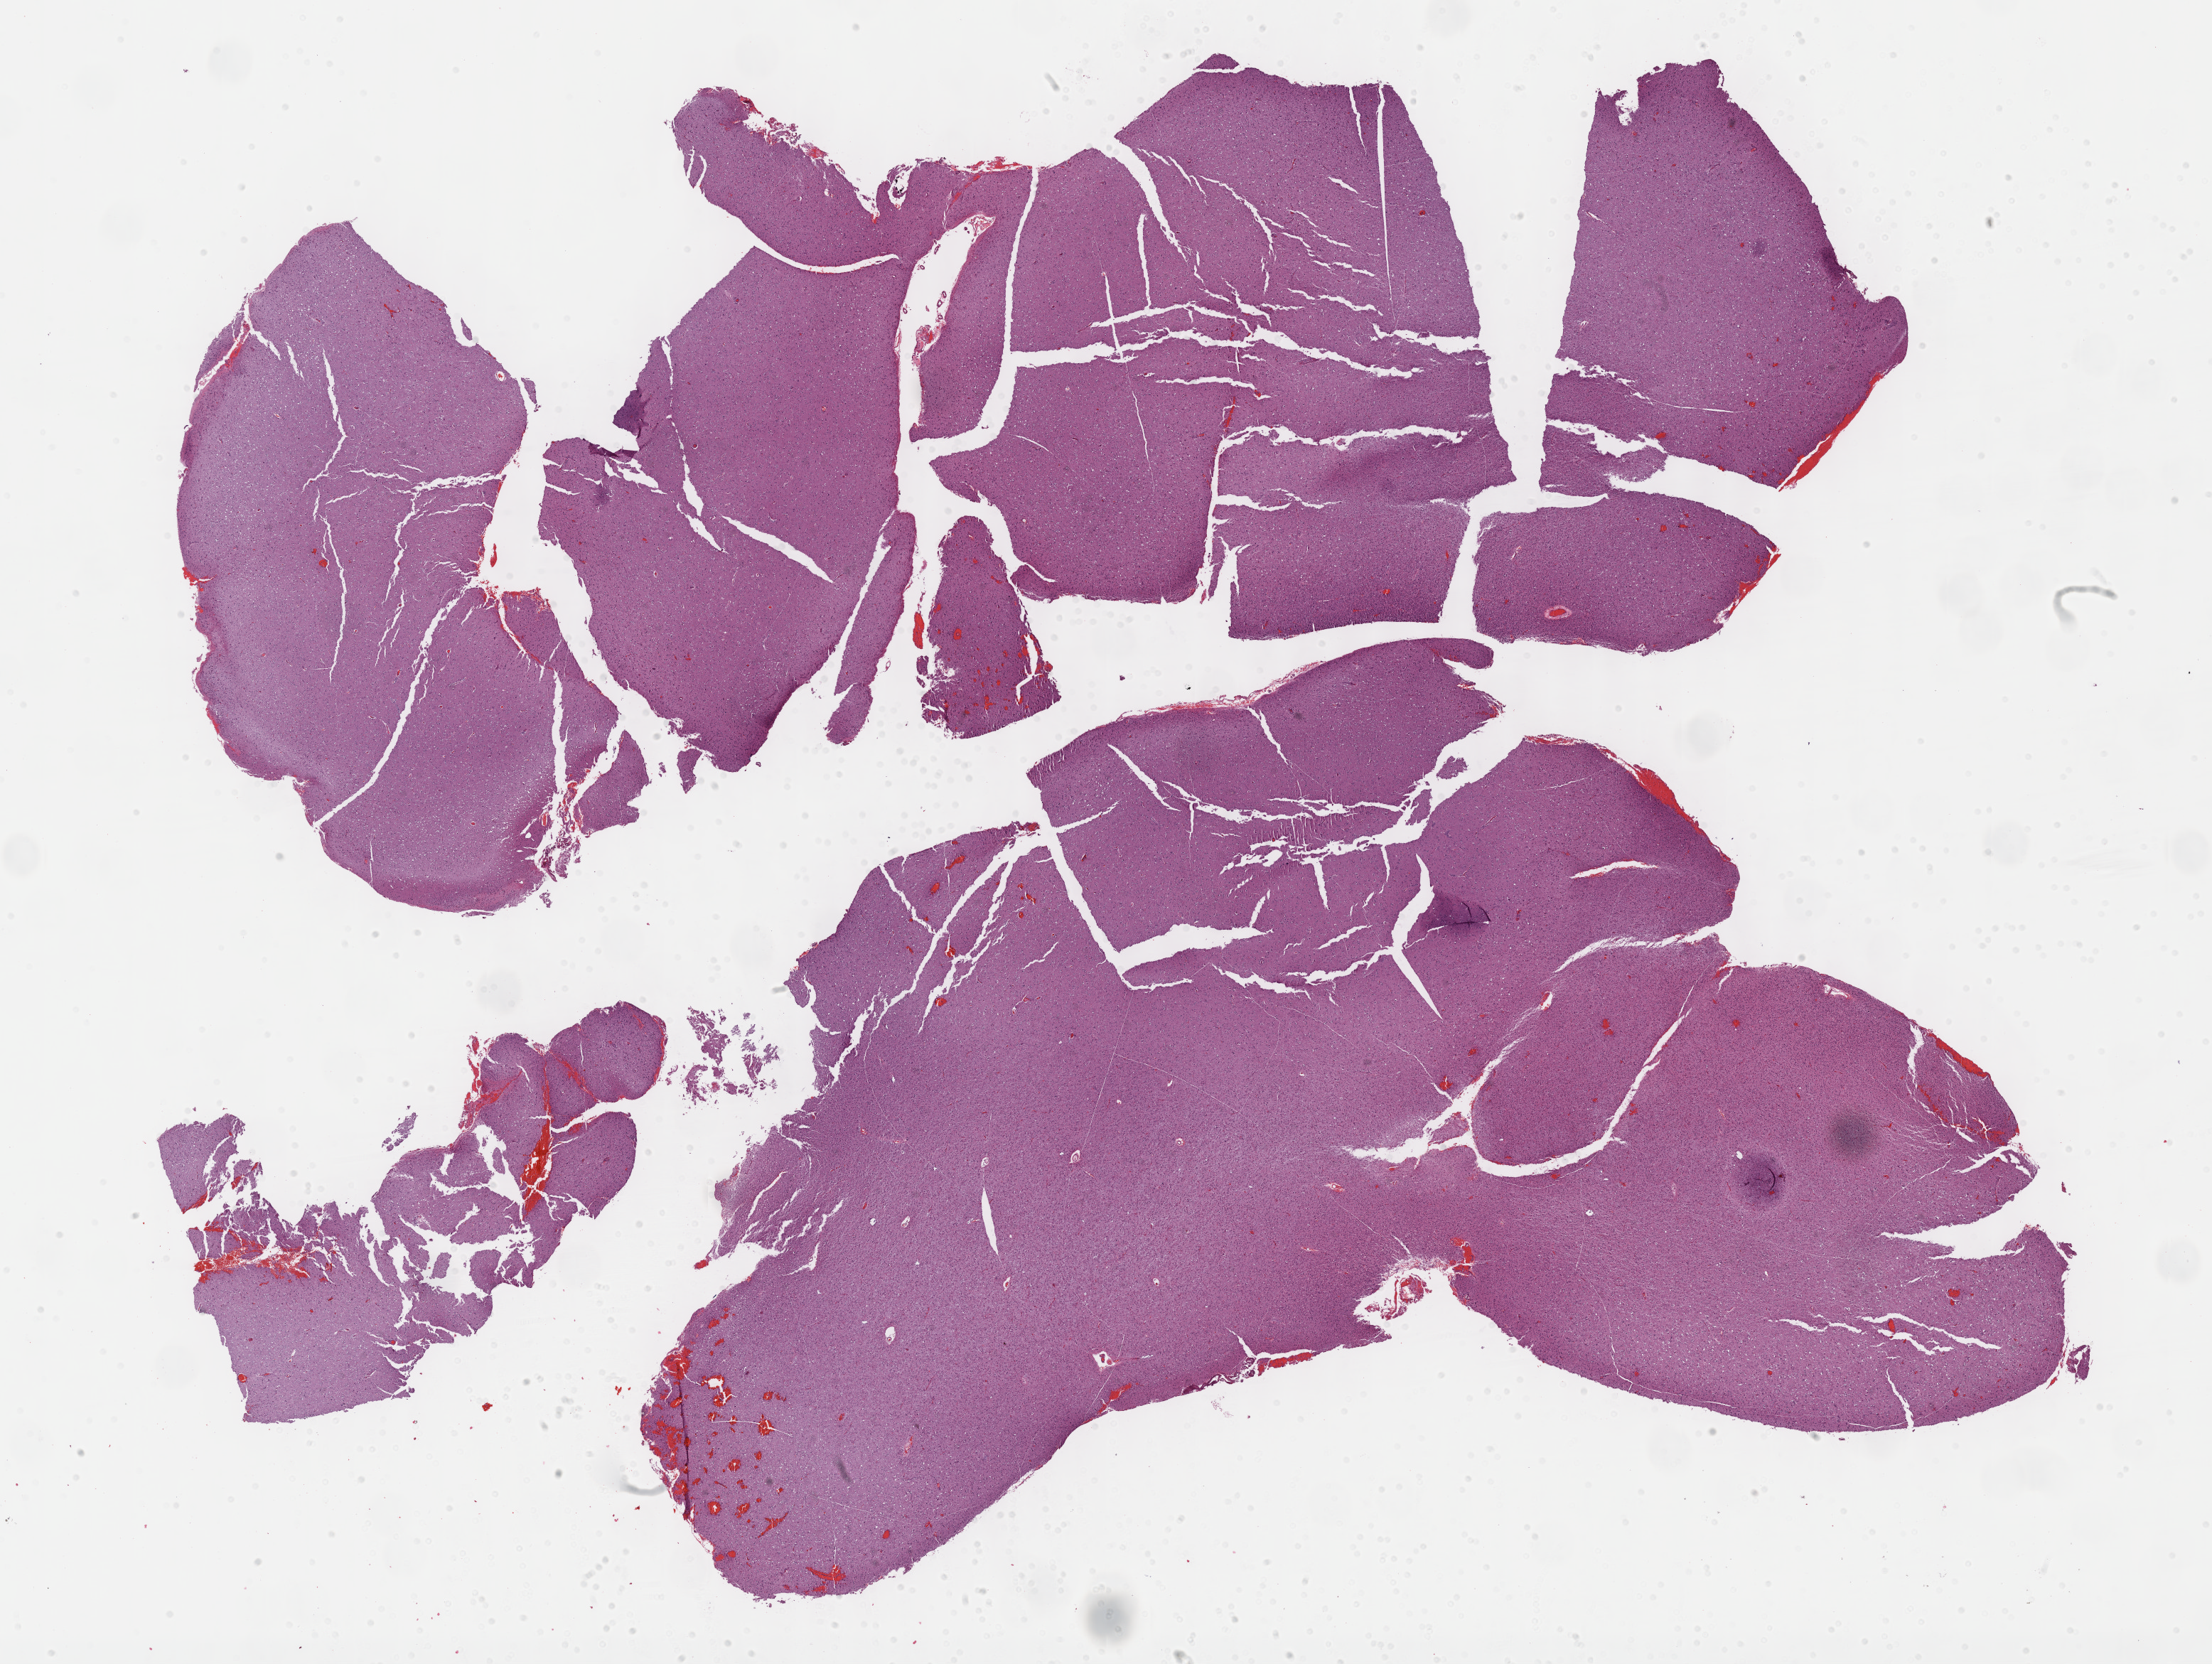
Whole-slide histology image, H&E — a low-resolution overview of the entire scanned area, about 25.2 x 18.9 mm. Formalin-fixed paraffin-embedded (FFPE) diagnostic section. Sample: primary tumour, brain. Male, age 28 years at initial diagnosis.
Pathologic diagnosis: Mixed glioma.